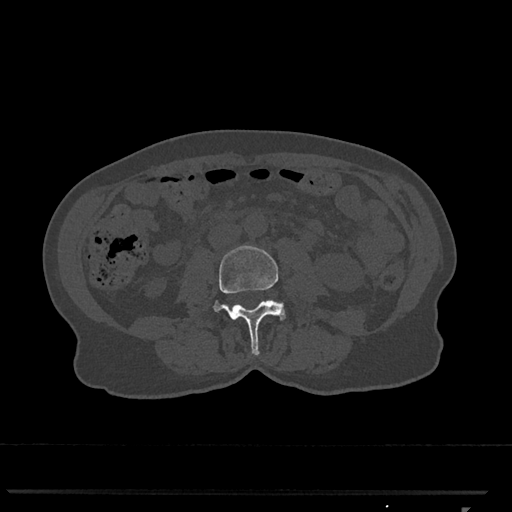
CT including the spine, one axial slice. Position 266 of 793 along the scan axis. Reconstruction kernel Br40s/3. 120 kVp. Bone window (W 1800 / L 400 HU). 512 × 512 image matrix. Patient: female, 62 years. Case-level facts recorded for this patient, not image findings: primary cancer: renal.
Outlined on this slice (semi-automatic segmentation, software-assisted and operator-edited):
- L3 vertebra: box from (x=213, y=245) to (x=286, y=355) px